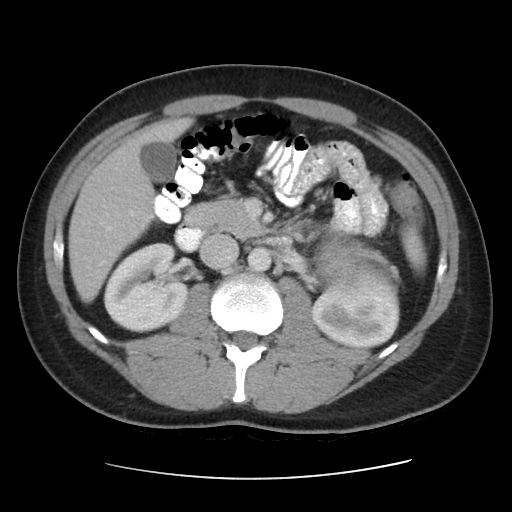
Contrast-enhanced abdominal CT, one axial slice. Slice 20 of 48 in the series (ordered by position). Reconstruction kernel STANDARD. 120 kVp. Intravenous contrast given. Soft-tissue window (W 400 / L 40 HU). 512 × 512 image matrix. Patient: male, 32 years. Case-level facts recorded for this patient, not image findings: diagnosis: adrenocortical carcinoma; tumour side: left adrenal; tumour size at pathology: 14 cm; Ki-67 index: 67 %; stage (as recorded): 3.
Structures marked on this image (semi-automatically segmented with operator editing):
- mass: bounding box [x1, y1, x2, y2] px = [318, 237, 388, 283]